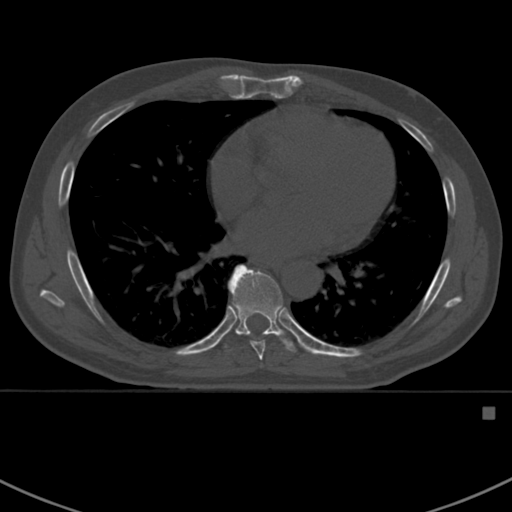
CT including the spine, one axial slice. Position 407 of 412 along the scan axis. Reconstruction kernel Br40s. 120 kVp. Bone window (W 1800 / L 400 HU). 1.5 mm slice thickness. 512 × 512 image matrix, field of view 358 × 358 mm. Male patient, age 59 years. From the clinical record (not read from this slice): primary cancer: prostate.
Outlined on this slice (semi-automatically segmented with operator editing):
- T7 vertebra: box from (x=251, y=342) to (x=265, y=365) px
- T8 vertebra: (x=223, y=265)–(x=300, y=353)